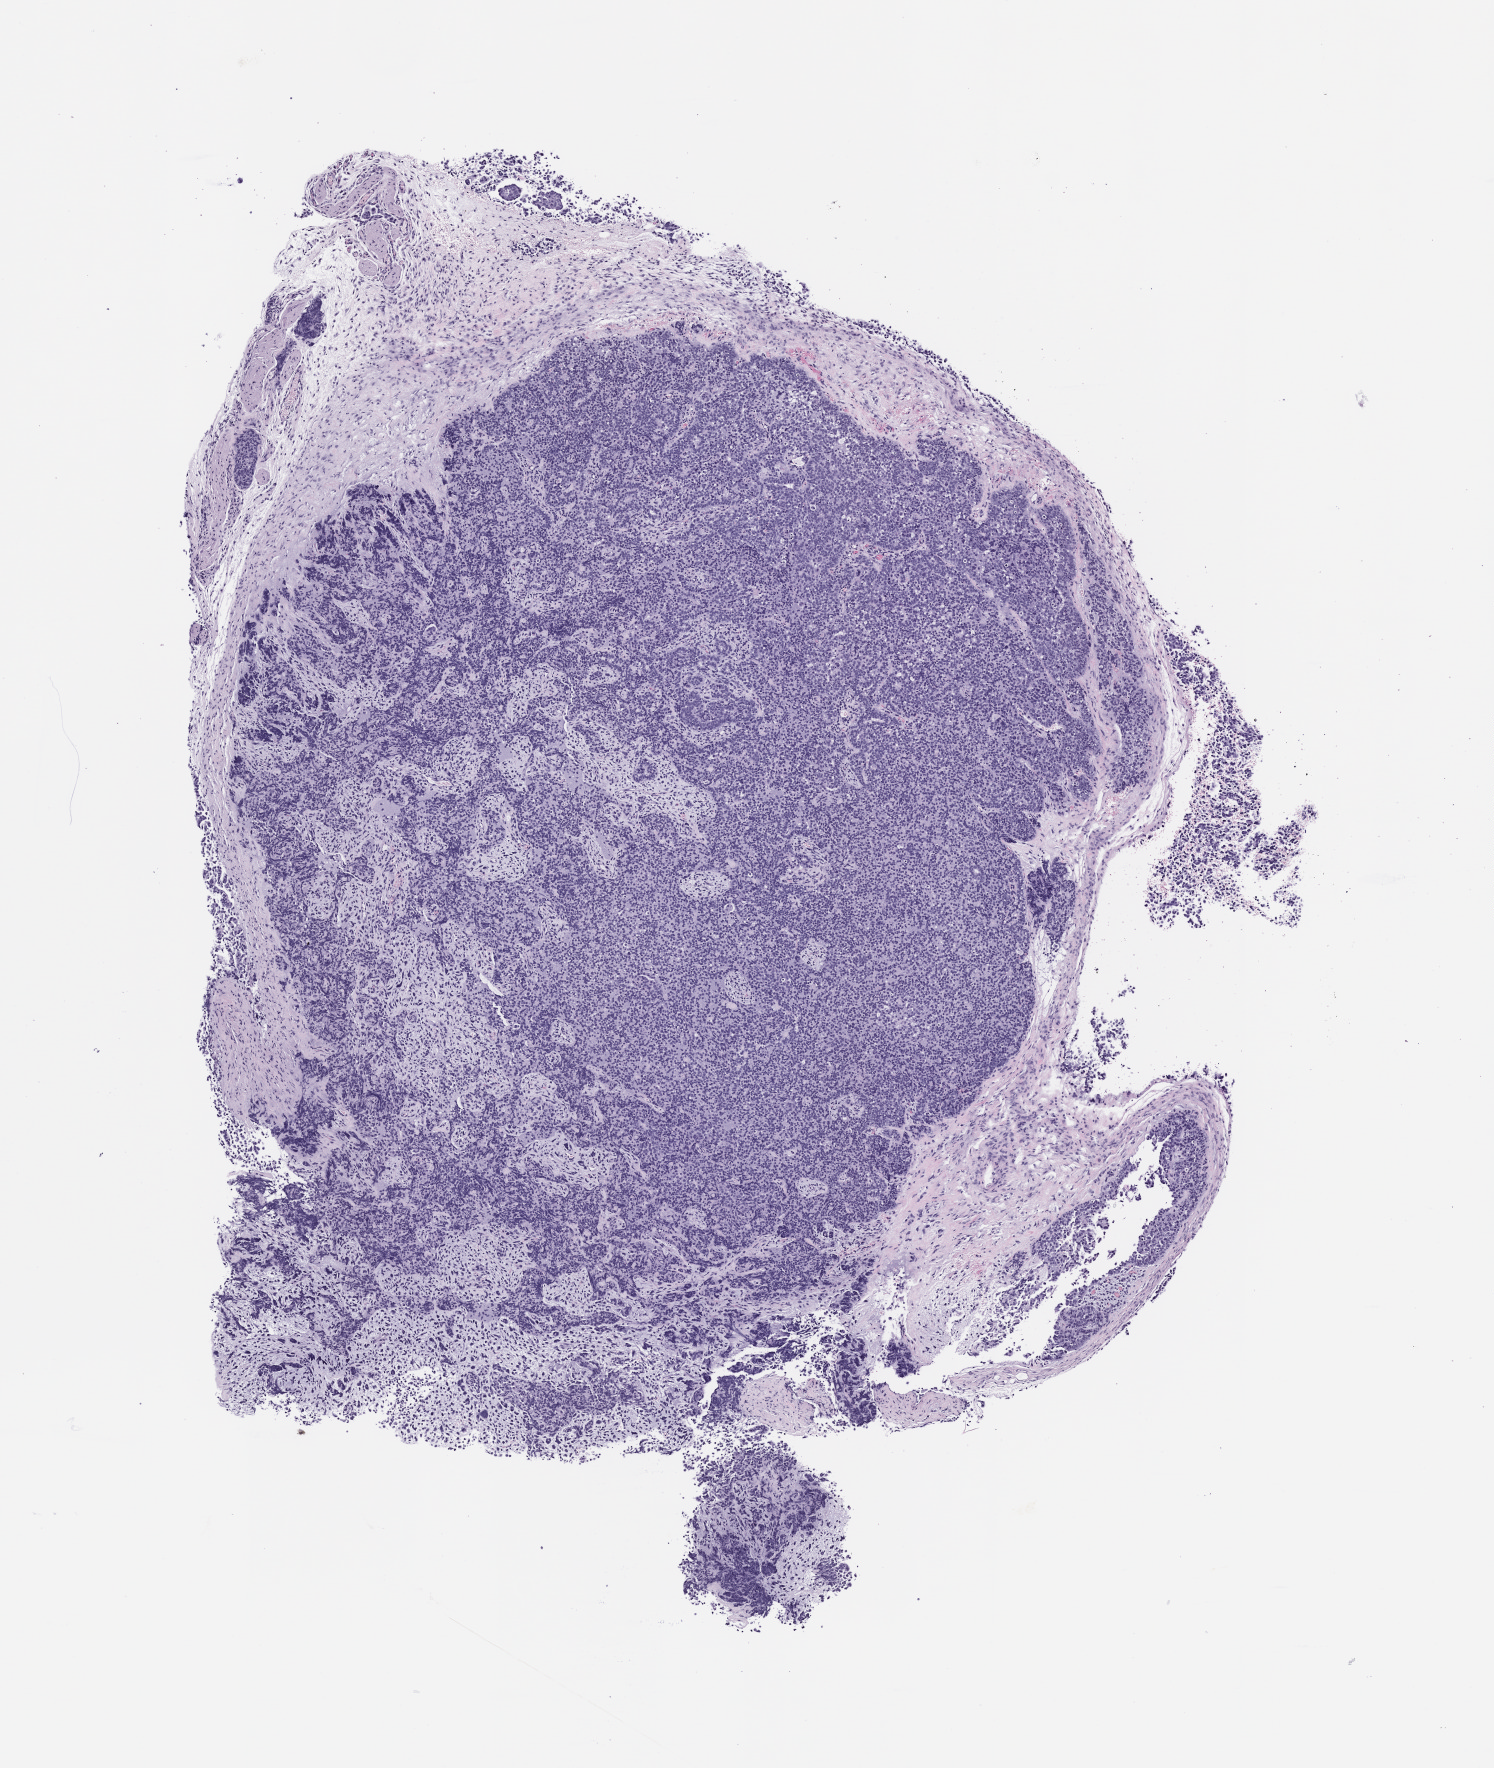
H&E whole-slide image of a patient-derived xenograft (PDX) tumor grown in a mouse, passage 2 — whole scanned area (about 6.0 x 7.1 mm) shown as a low-resolution overview, formalin-fixed paraffin-embedded section, tumor site category: uterus.
Originating patient diagnosis: Carcinosarcoma.